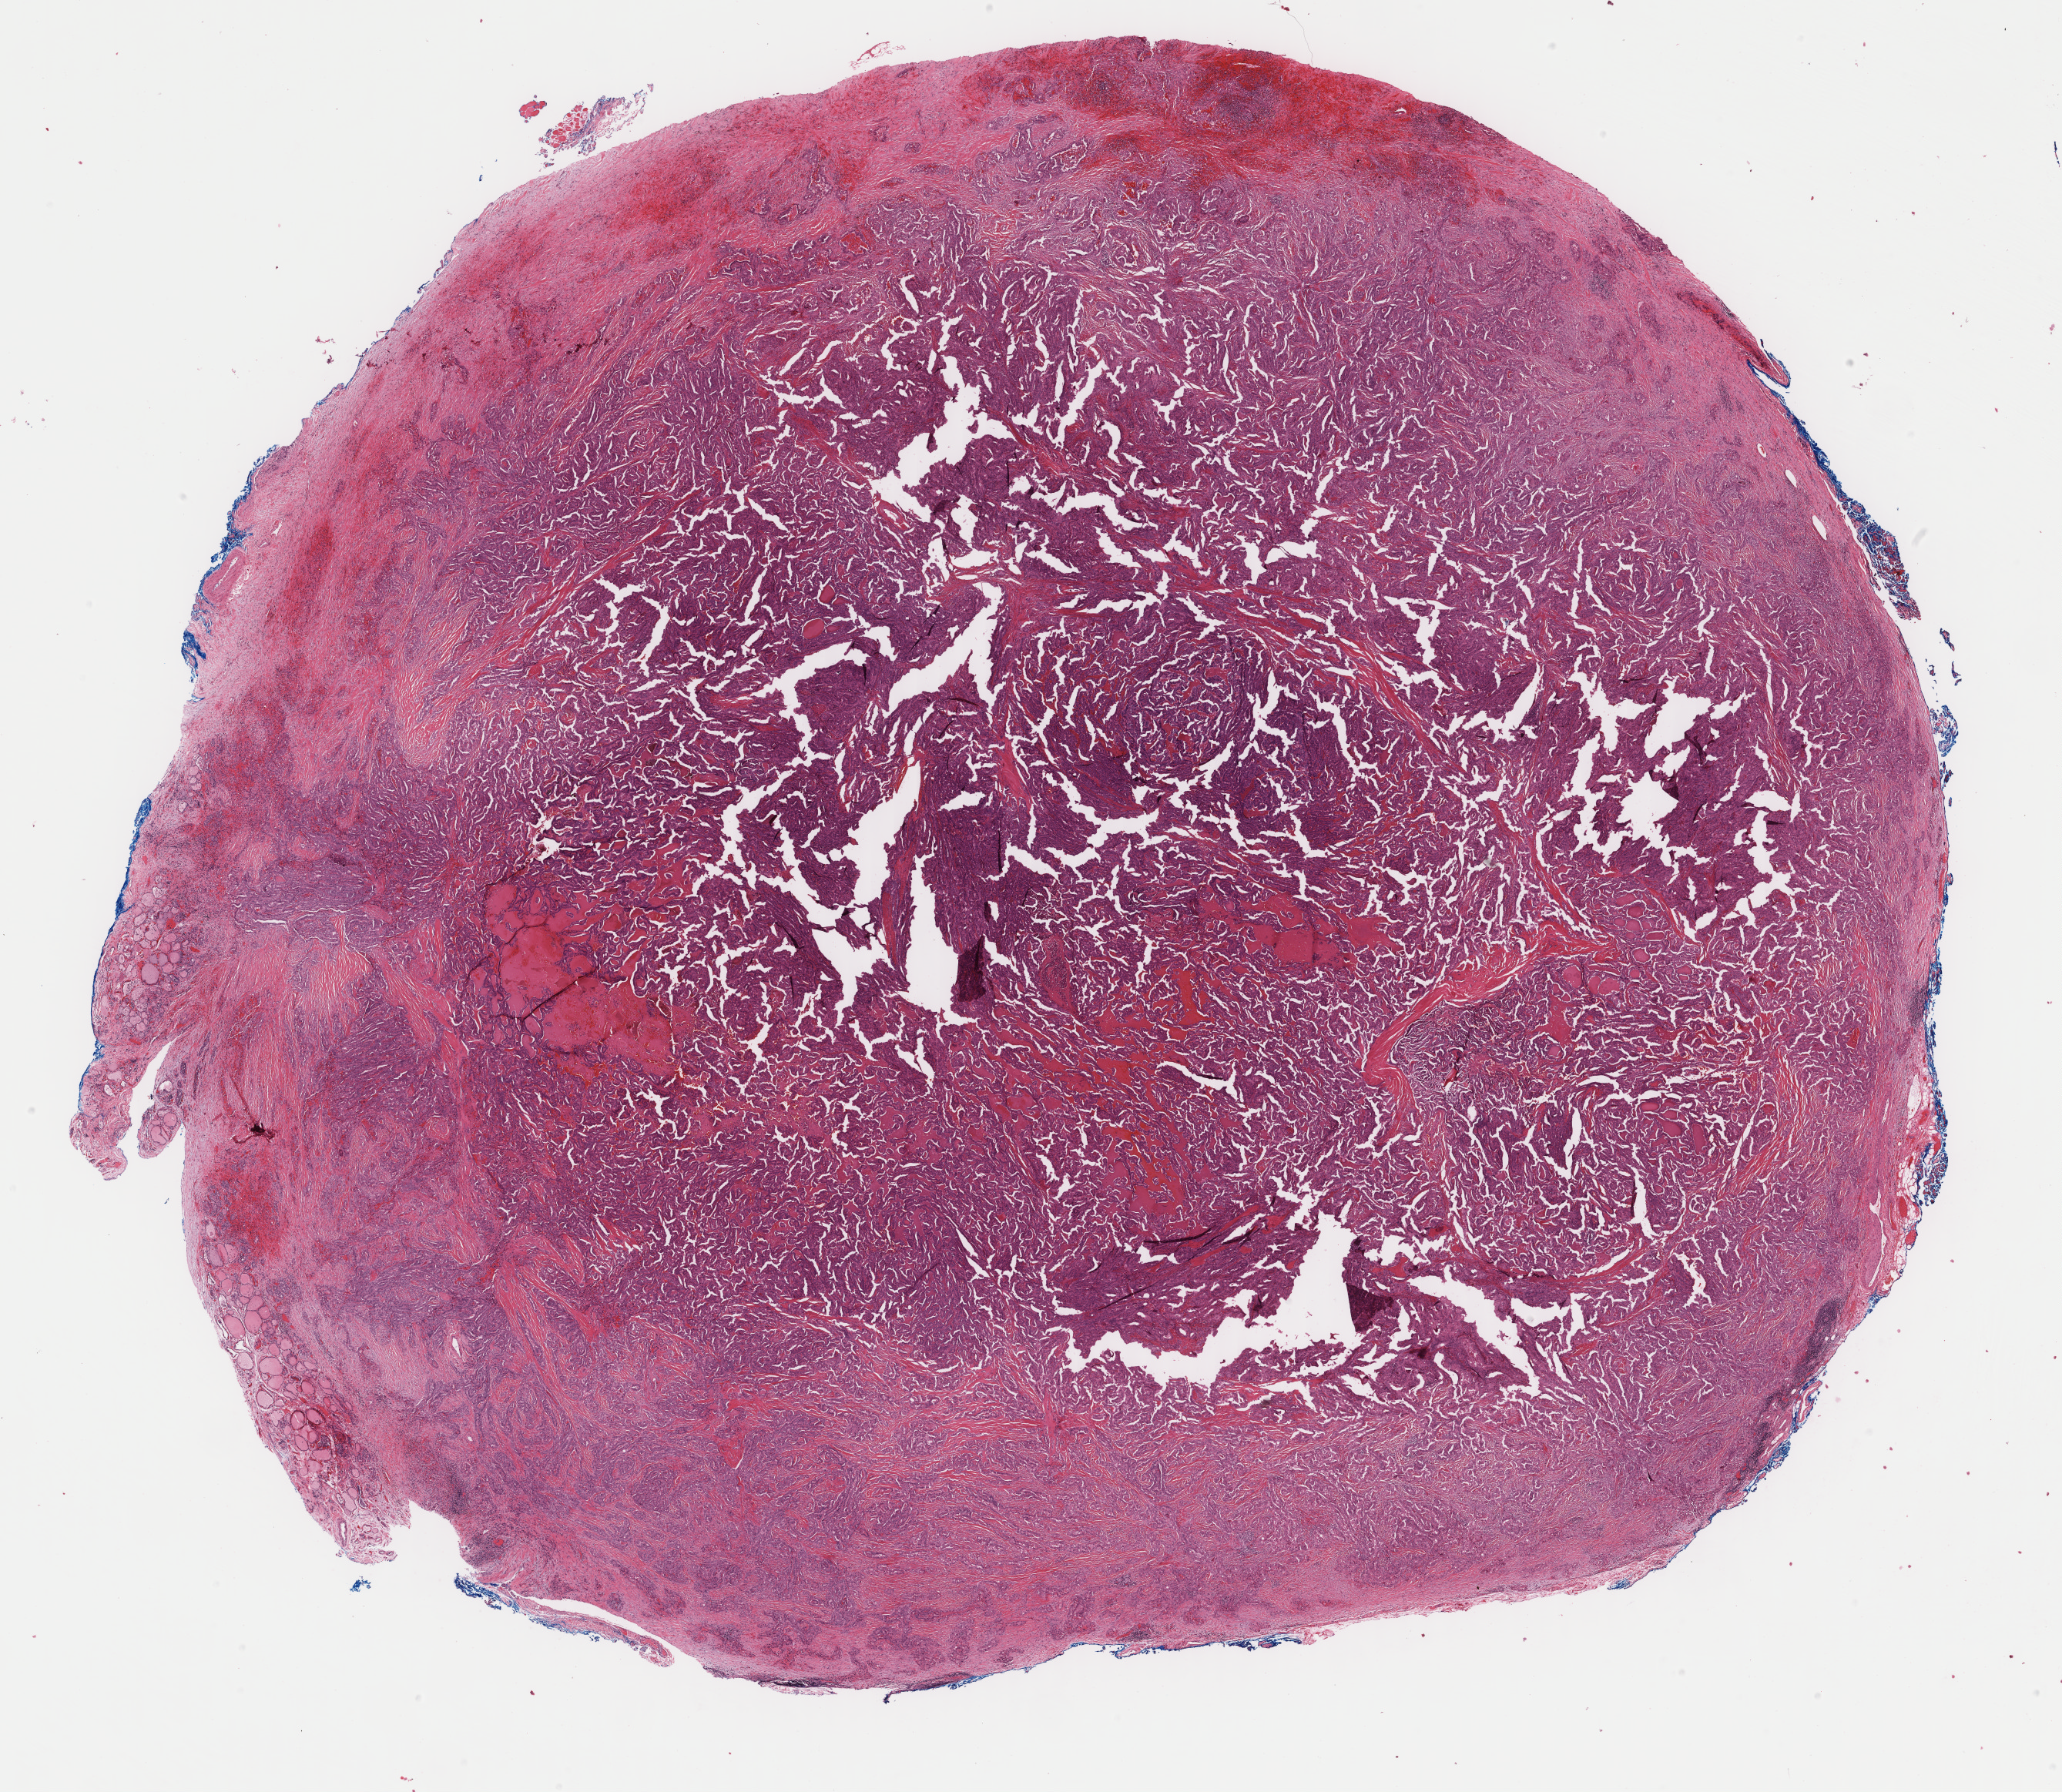
Whole-slide histology image, H&E, a low-resolution overview of the entire scanned area, about 21.2 x 18.5 mm (acquisition: 40x scan), formalin-fixed paraffin-embedded (FFPE) diagnostic section, sample: primary tumour, thyroid. Male patient; age at initial diagnosis 52 years.
Pathologic diagnosis: Papillary adenocarcinoma, NOS (thyroid gland).